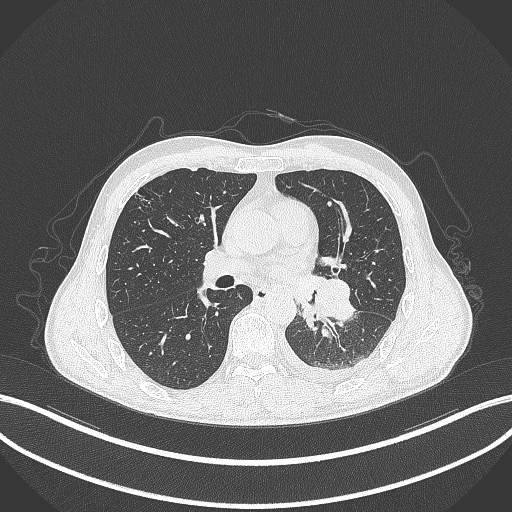
Chest CT, one axial slice. Slice 171 of 295 in the series (ordered by position). Reconstruction kernel B70f. Lung window (W 1500 / L -600 HU). 512 × 512 image matrix, field of view 400 × 400 mm. Patient: male, 47 years. From the clinical record (not read from this slice): clinical TNM (as recorded): T3 N1 M1c; histopathological grade: G3.
Outlined on this slice (bounding box drawn by a radiologist):
- lung tumour (recorded histology: small cell carcinoma): bounding box [x1, y1, x2, y2] px = [309, 276, 357, 325]